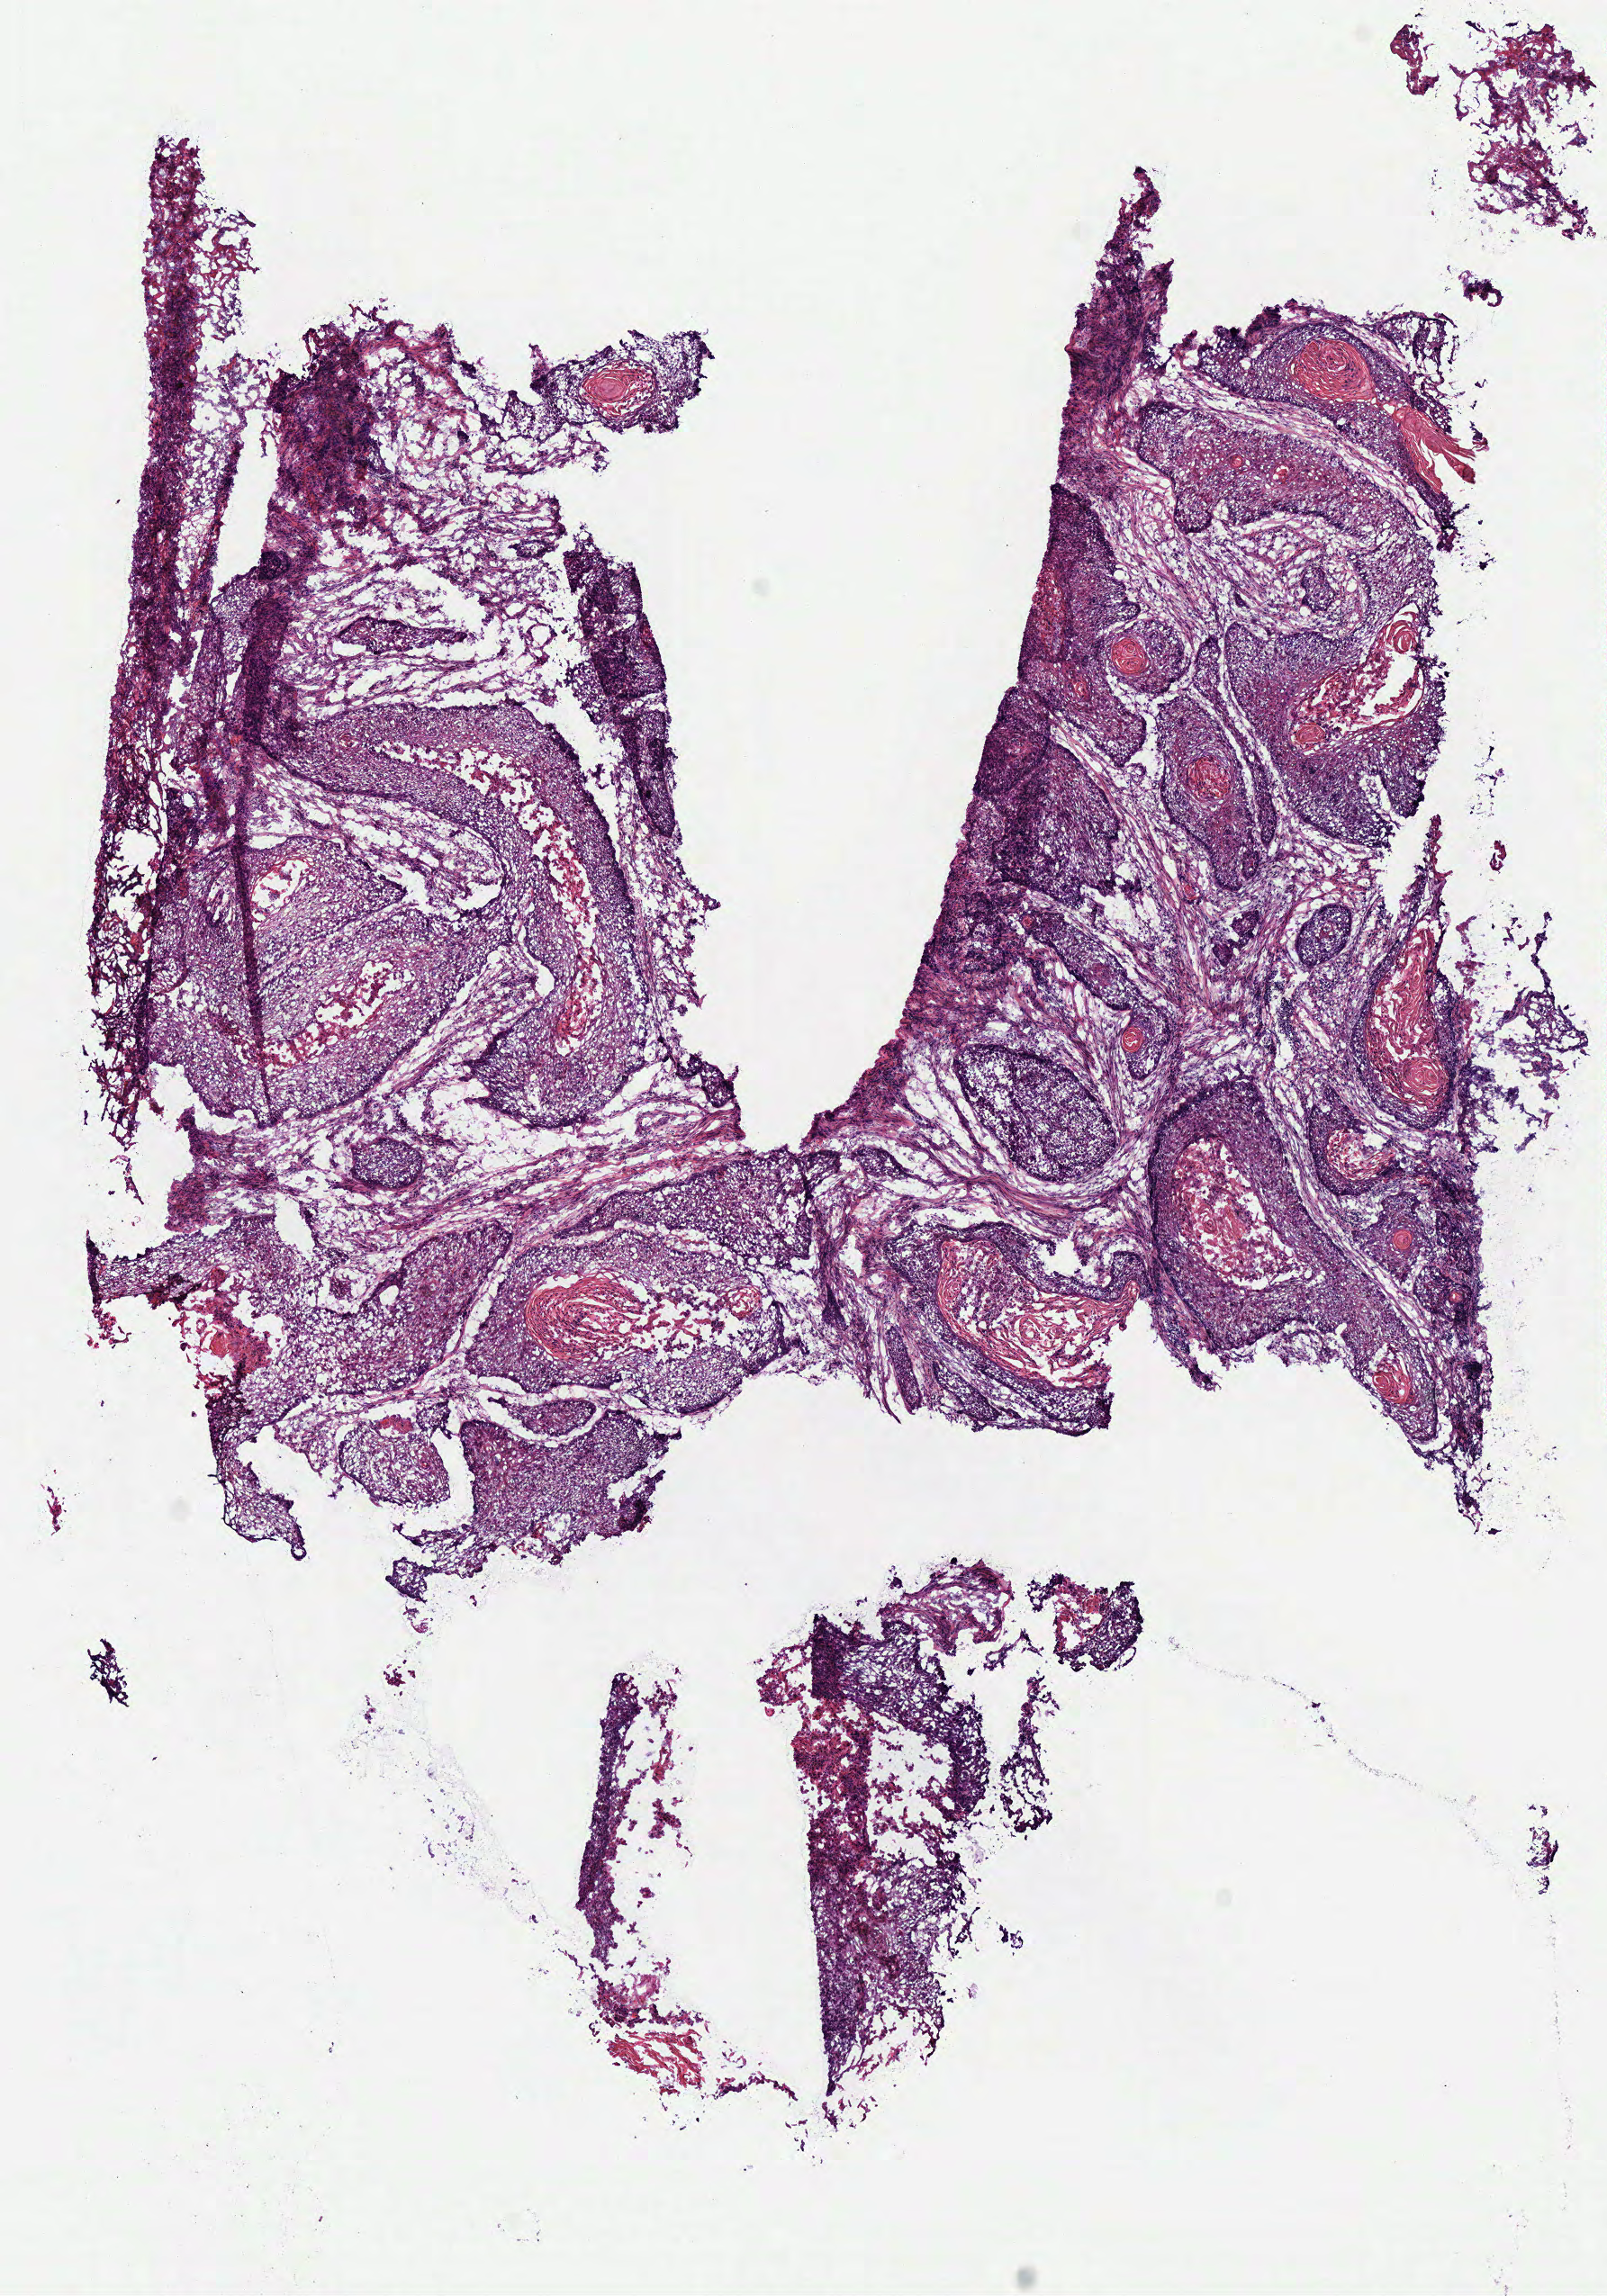
H&E-stained whole-slide image — low-resolution overview of the scanned area, about 7.0 x 10.0 mm (from a 40x scan). Frozen section from the top of the tissue portion. Primary tumour sample from the head and neck. Female, age 53 years at initial diagnosis. Composition of this section per pathologist review: tumour cells 85%, tumour nuclei 80%.
Diagnosis: Squamous cell carcinoma, NOS.